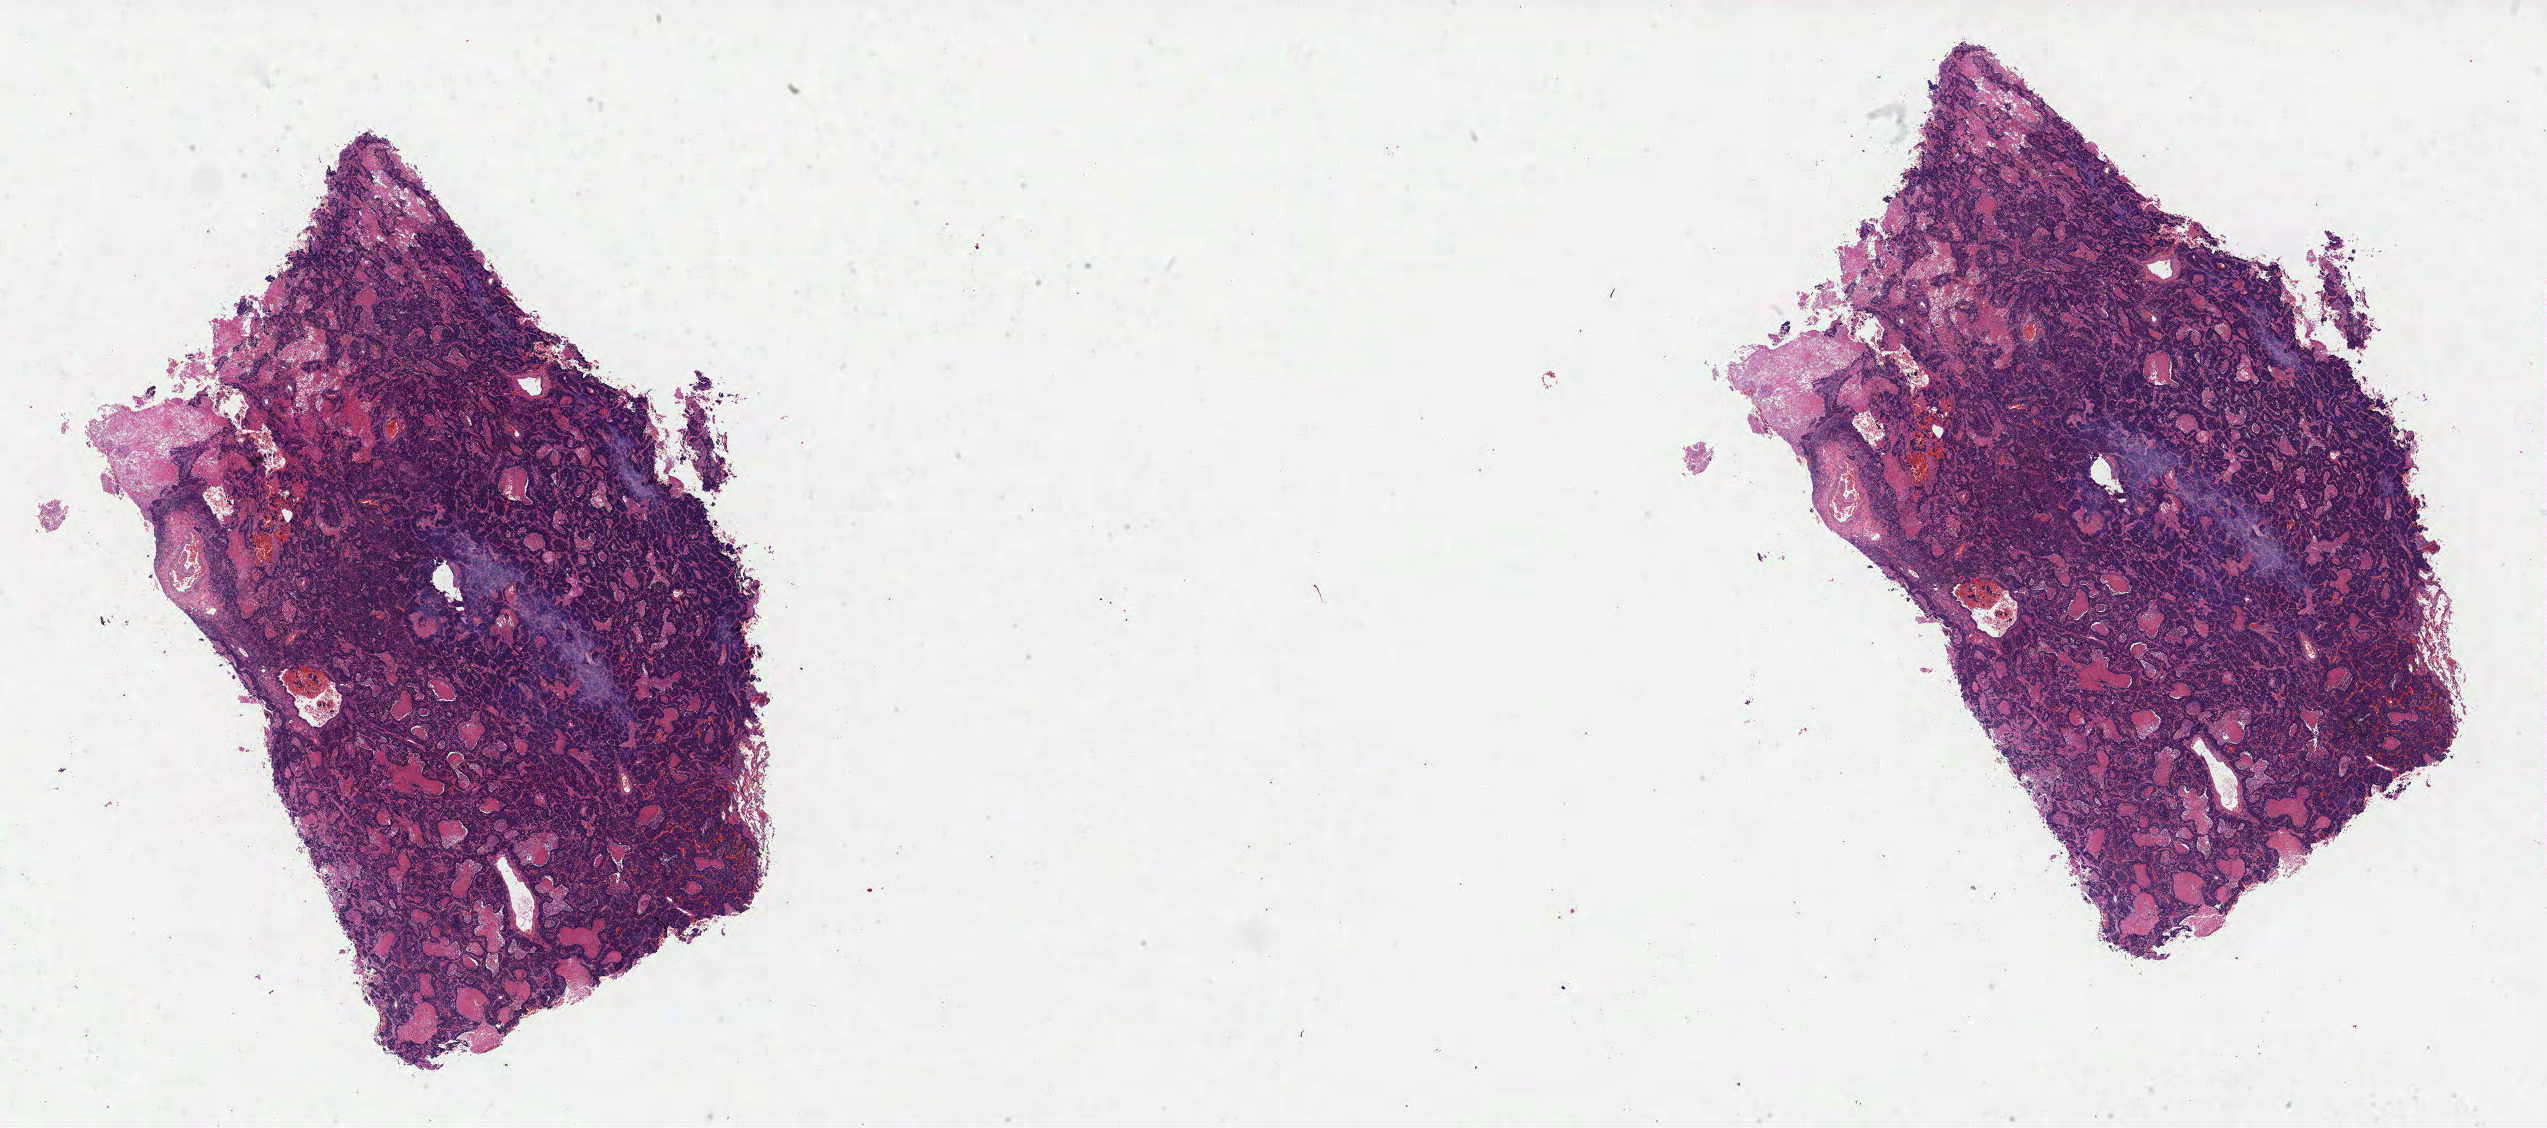
Digitized Hematoxylin and eosin (H&E) stained tissue section (whole slide) — low-resolution overview of the scanned area, about 41.1 x 18.2 mm (slide scanned at 40x); formalin-fixed paraffin-embedded (FFPE) diagnostic section; primary tumour sample from the lung. Male patient; age at initial diagnosis 68 years.
AJCC pathologic stage: IB (7th edition). Laterality: right. Histologic diagnosis: Squamous cell carcinoma, NOS.